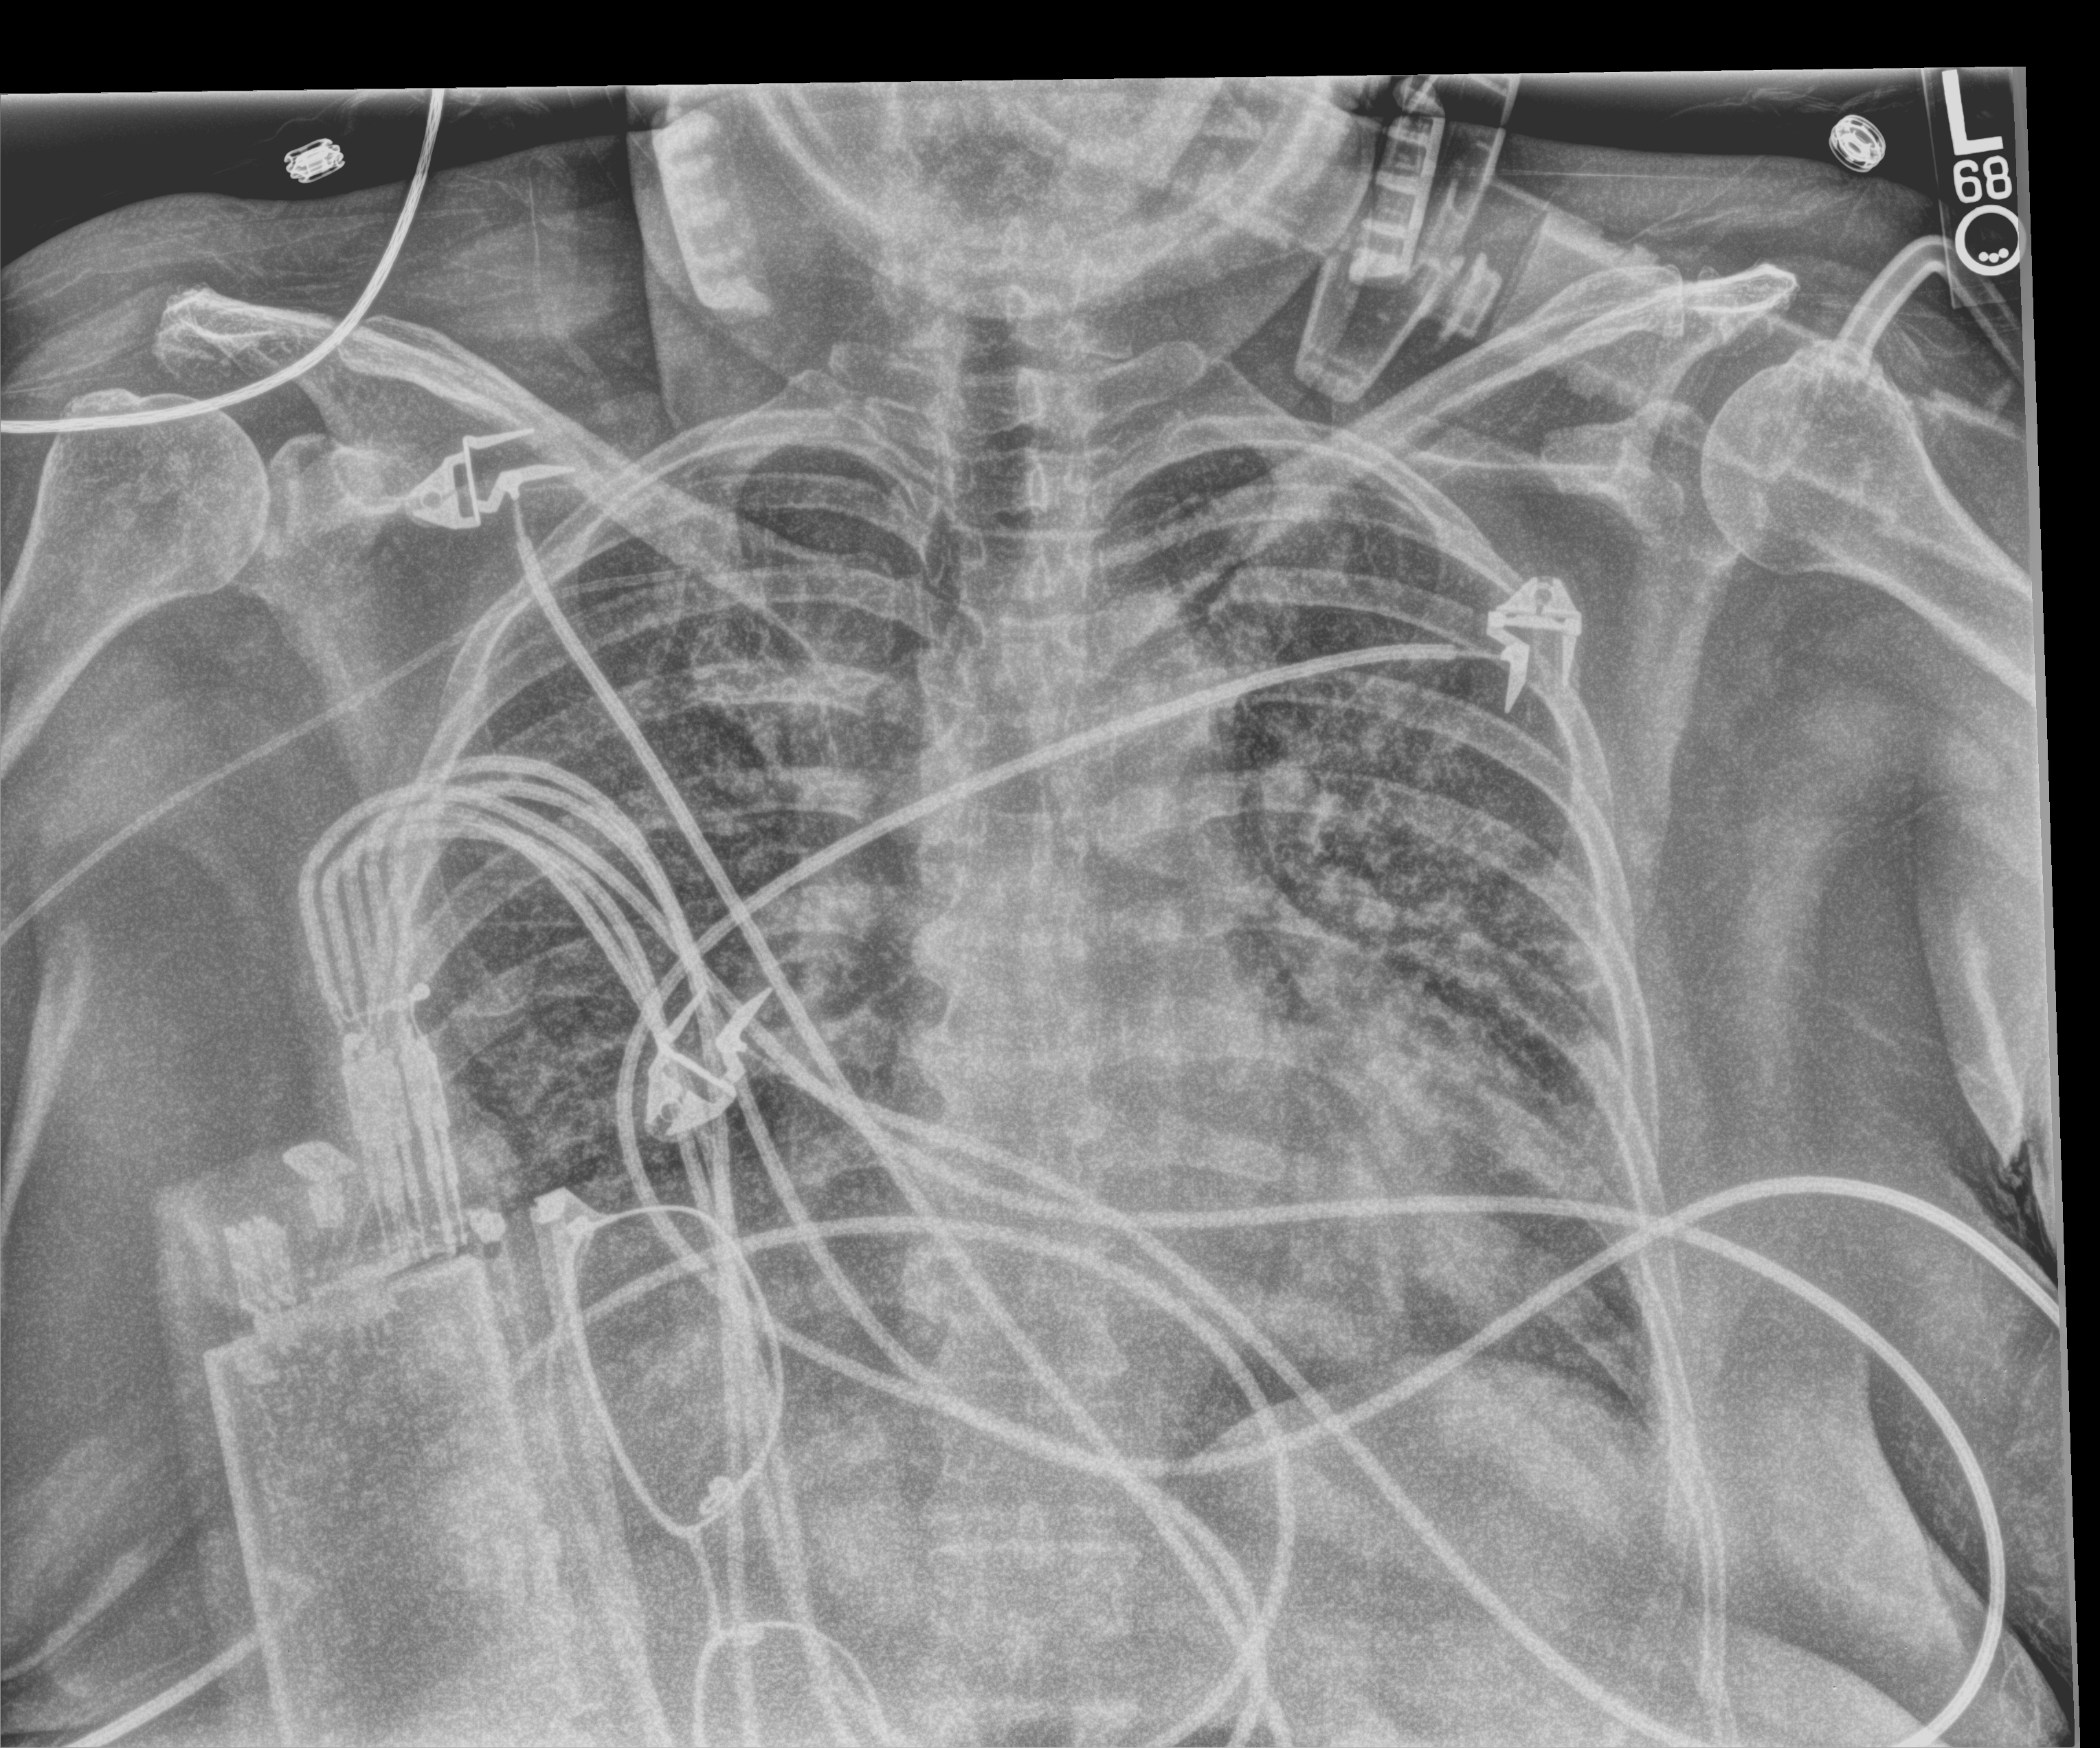
Portable chest radiograph, anteroposterior (AP) projection. Female patient hospitalised with COVID-19, age 60–74 years.
From the hospital-stay record, not from the radiograph (when in the stay this image was taken is not recorded):
- mechanically ventilated during this hospital stay: yes